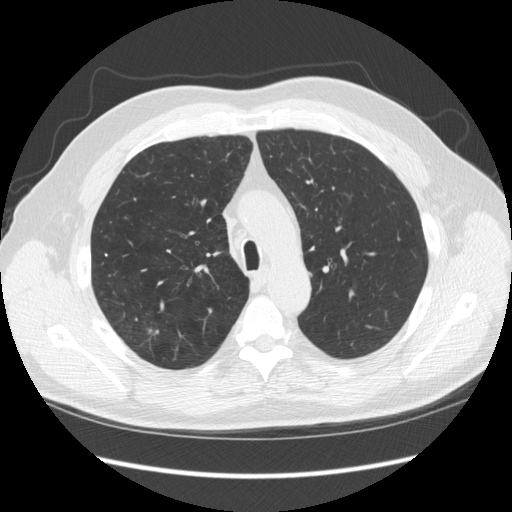
Low-dose screening chest CT, one axial slice. Position 177 of 248 along the scan axis. Reconstruction kernel STANDARD. 120 kVp. Lung window (W 1500 / L -600 HU). 512 × 512 image matrix, field of view 380 × 380 mm.
Annotated regions visible in this slice (manually delineated by an expert):
- lesion 1 (tumor, upper lobe of right lung): bounding box [x1, y1, x2, y2] px = [146, 328, 153, 335]